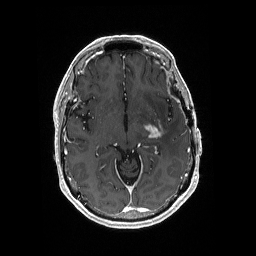
Brain MRI from a brain-tumour surgery series, one axial slice. Position 107 of 176 along the scan axis. T1-weighted post-contrast. 1 mm slice thickness. 256 × 256 image matrix, field of view 256 × 256 mm. From the clinical record (not read from this slice): histopathology: Glioblastoma; WHO grade: 4; IDH mutation: no; tumour location: Left Medial Temporal.
Annotated regions visible in this slice (manually delineated by an expert):
- tumour: bounding box (x1, y1, x2, y2) in pixels: (143, 119, 170, 140)